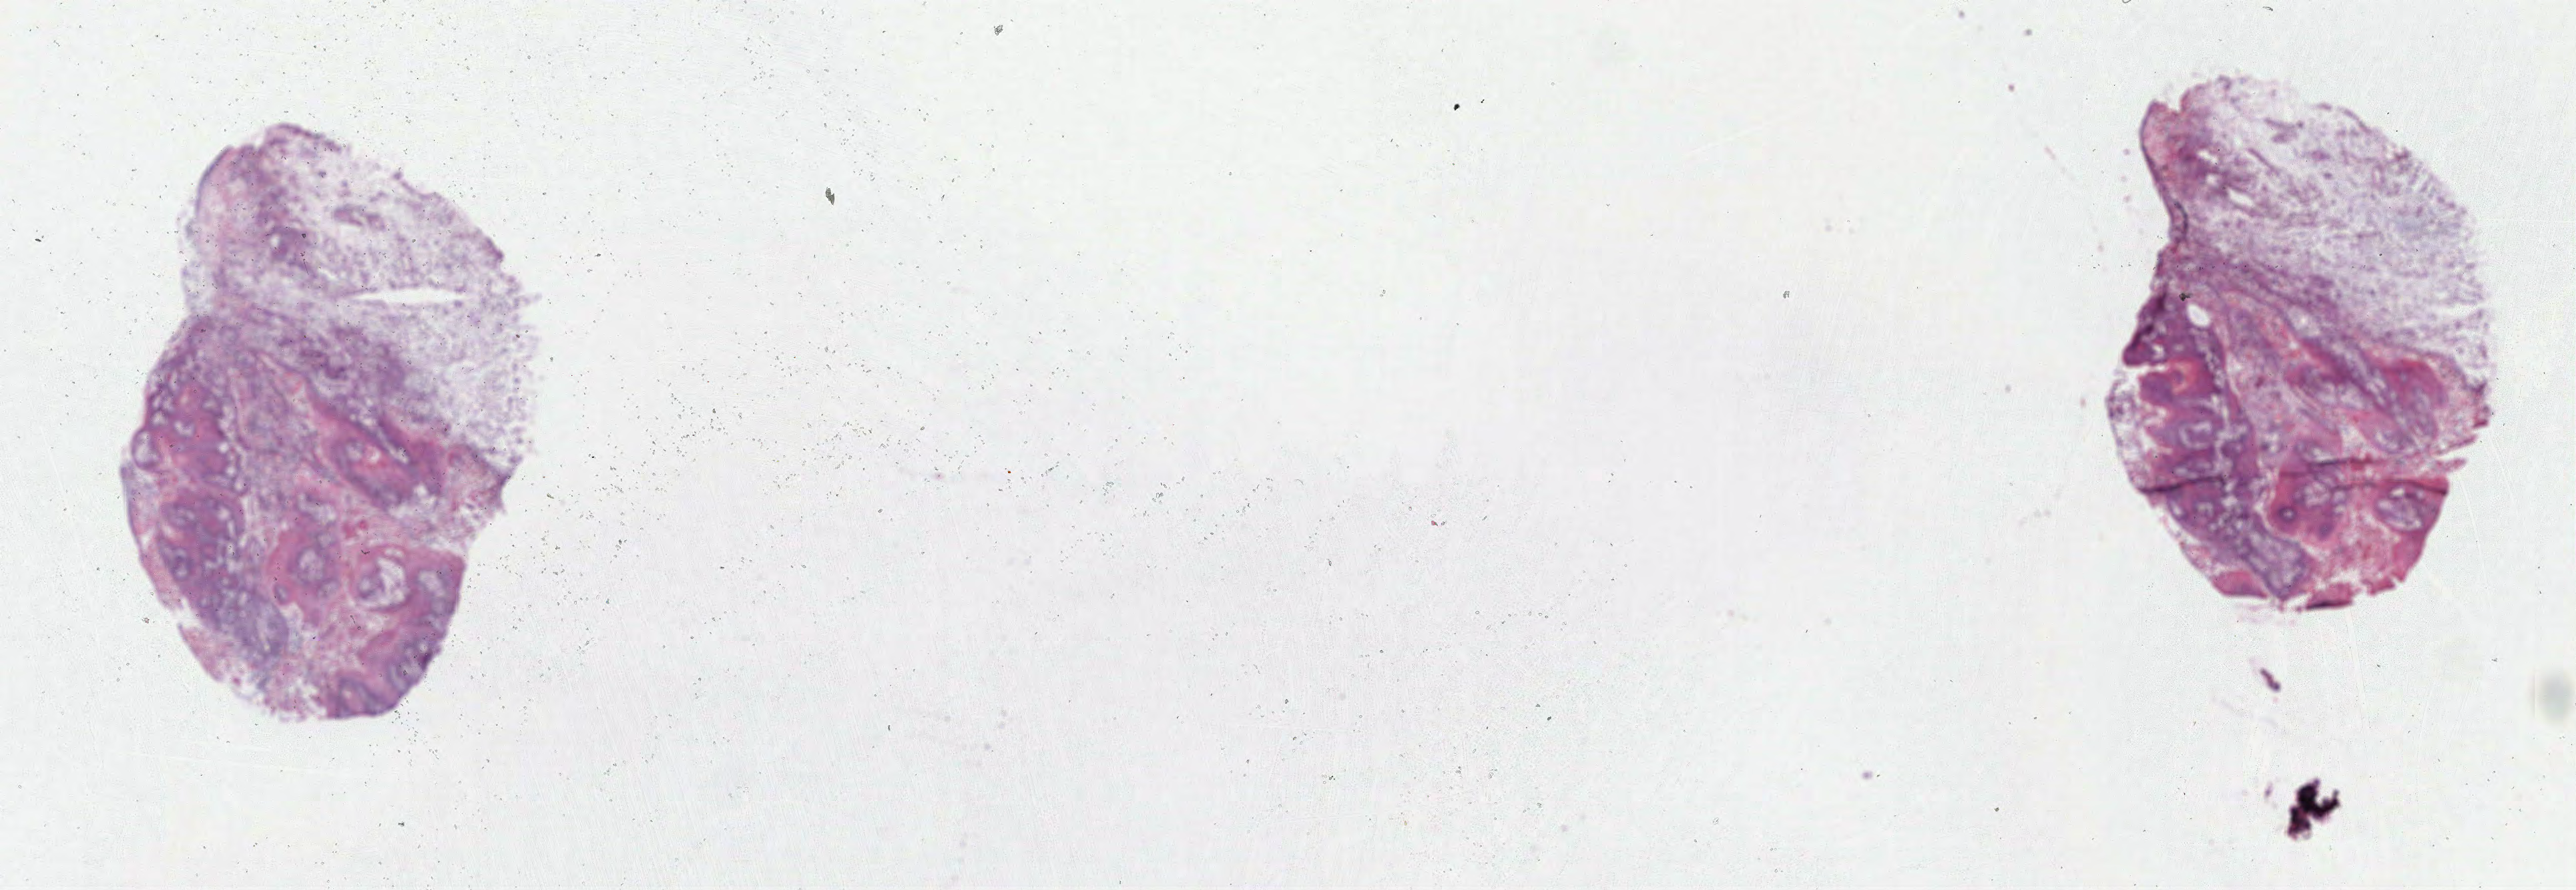
H&E-stained whole-slide image, whole scanned area (about 30.3 x 10.5 mm) shown as a low-resolution overview. Formalin-fixed paraffin-embedded (FFPE) diagnostic section. Primary tumour sample from the head and neck. Female patient; age at initial diagnosis 41 years. Histologic grade: G2 (moderately differentiated).
TNM: T1 N1. Pathologic diagnosis: Squamous cell carcinoma, NOS. Lymph nodes positive (case pathology): 1 of 34 examined. AJCC pathologic stage: III (7th edition).